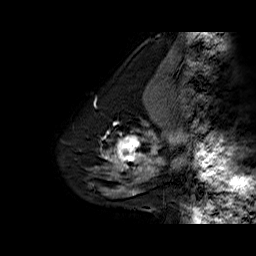
Breast MRI (dynamic contrast-enhanced), one sagittal slice. Position 16 of 60 along the scan axis. Dynamic contrast-enhanced series, time point 2 of 6 at this slice position (early post-contrast). 1.5 T. TE 6.3 ms, TR 32.5 ms. 4 mm slice thickness. 256 × 256 image matrix, field of view 200 × 200 mm. Female patient. From the clinical record (not read from this slice): setting: breast cancer imaged before/during neoadjuvant chemotherapy; receptor status: triple-negative.
Structures marked on this image (semi-automatic segmentation, software-assisted and operator-edited):
- analysis volume of interest (the breast-tissue region the enhancement analysis was run in; not a lesion): box from (x=108, y=129) to (x=154, y=177) px
- tumour enhancement mask (voxels above the 100 % enhancement threshold inside the analysis volume of interest): (x=108, y=132)–(x=154, y=176)